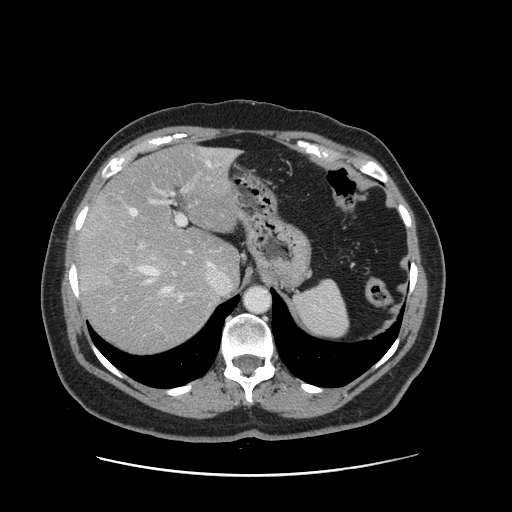
Contrast-enhanced abdominal CT, one axial slice; slice 109 of 161 in the series (ordered by position); 120 kVp; intravenous contrast given; soft-tissue window (W 400 / L 40 HU); 512 × 512 image matrix, field of view 398 × 398 mm. Female patient, age 62 years. From the clinical record (not read from this slice): diagnosis: colorectal cancer liver metastases, imaged before liver resection; multiple liver metastases: no.
Outlined on this slice (expert manual segmentation):
- hepatic veins: bounding box <131,162,229,294> (left, top, right, bottom; pixels)
- liver: <80,147,239,354>
- planned liver remnant (the part of the liver to remain after resection): <99,147,238,279>
- portal vein (with intrahepatic branches): <112,173,202,312>
- liver metastasis: <108,265,132,290>